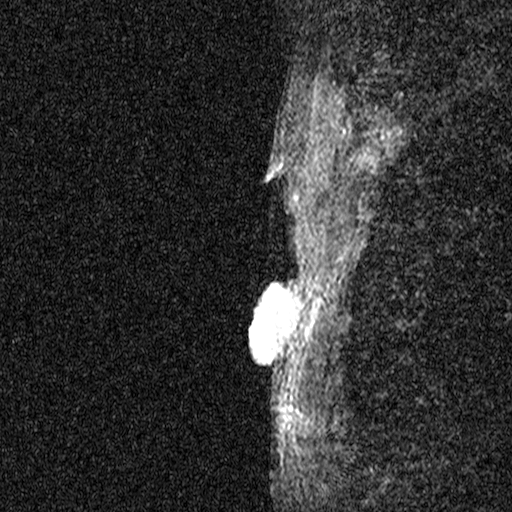
Breast MRI (dynamic contrast-enhanced), one sagittal slice. Position 42 of 44 along the scan axis. Dynamic contrast-enhanced study with each time point stored as its own series, time point 2 of 3 at this slice position (early post-contrast, ordered by acquisition time). 1.5 T. TE 4.5 ms, TR 11 ms. 2.05 mm slice thickness. 512 × 512 image matrix, field of view 200 × 200 mm. Patient: female, 44 years. Case-level facts recorded for this patient, not image findings: setting: breast cancer imaged before/during neoadjuvant chemotherapy; receptor status: HR-positive, HER2-negative.
Structures marked on this image (semi-automatically segmented with operator editing):
- analysis volume of interest (the breast-tissue region the enhancement analysis was run in; not a lesion): bounding box [x1, y1, x2, y2] px = [204, 254, 317, 401]
- tumour enhancement mask (voxels above the 90 % enhancement threshold inside the analysis volume of interest): [249, 291, 271, 364]